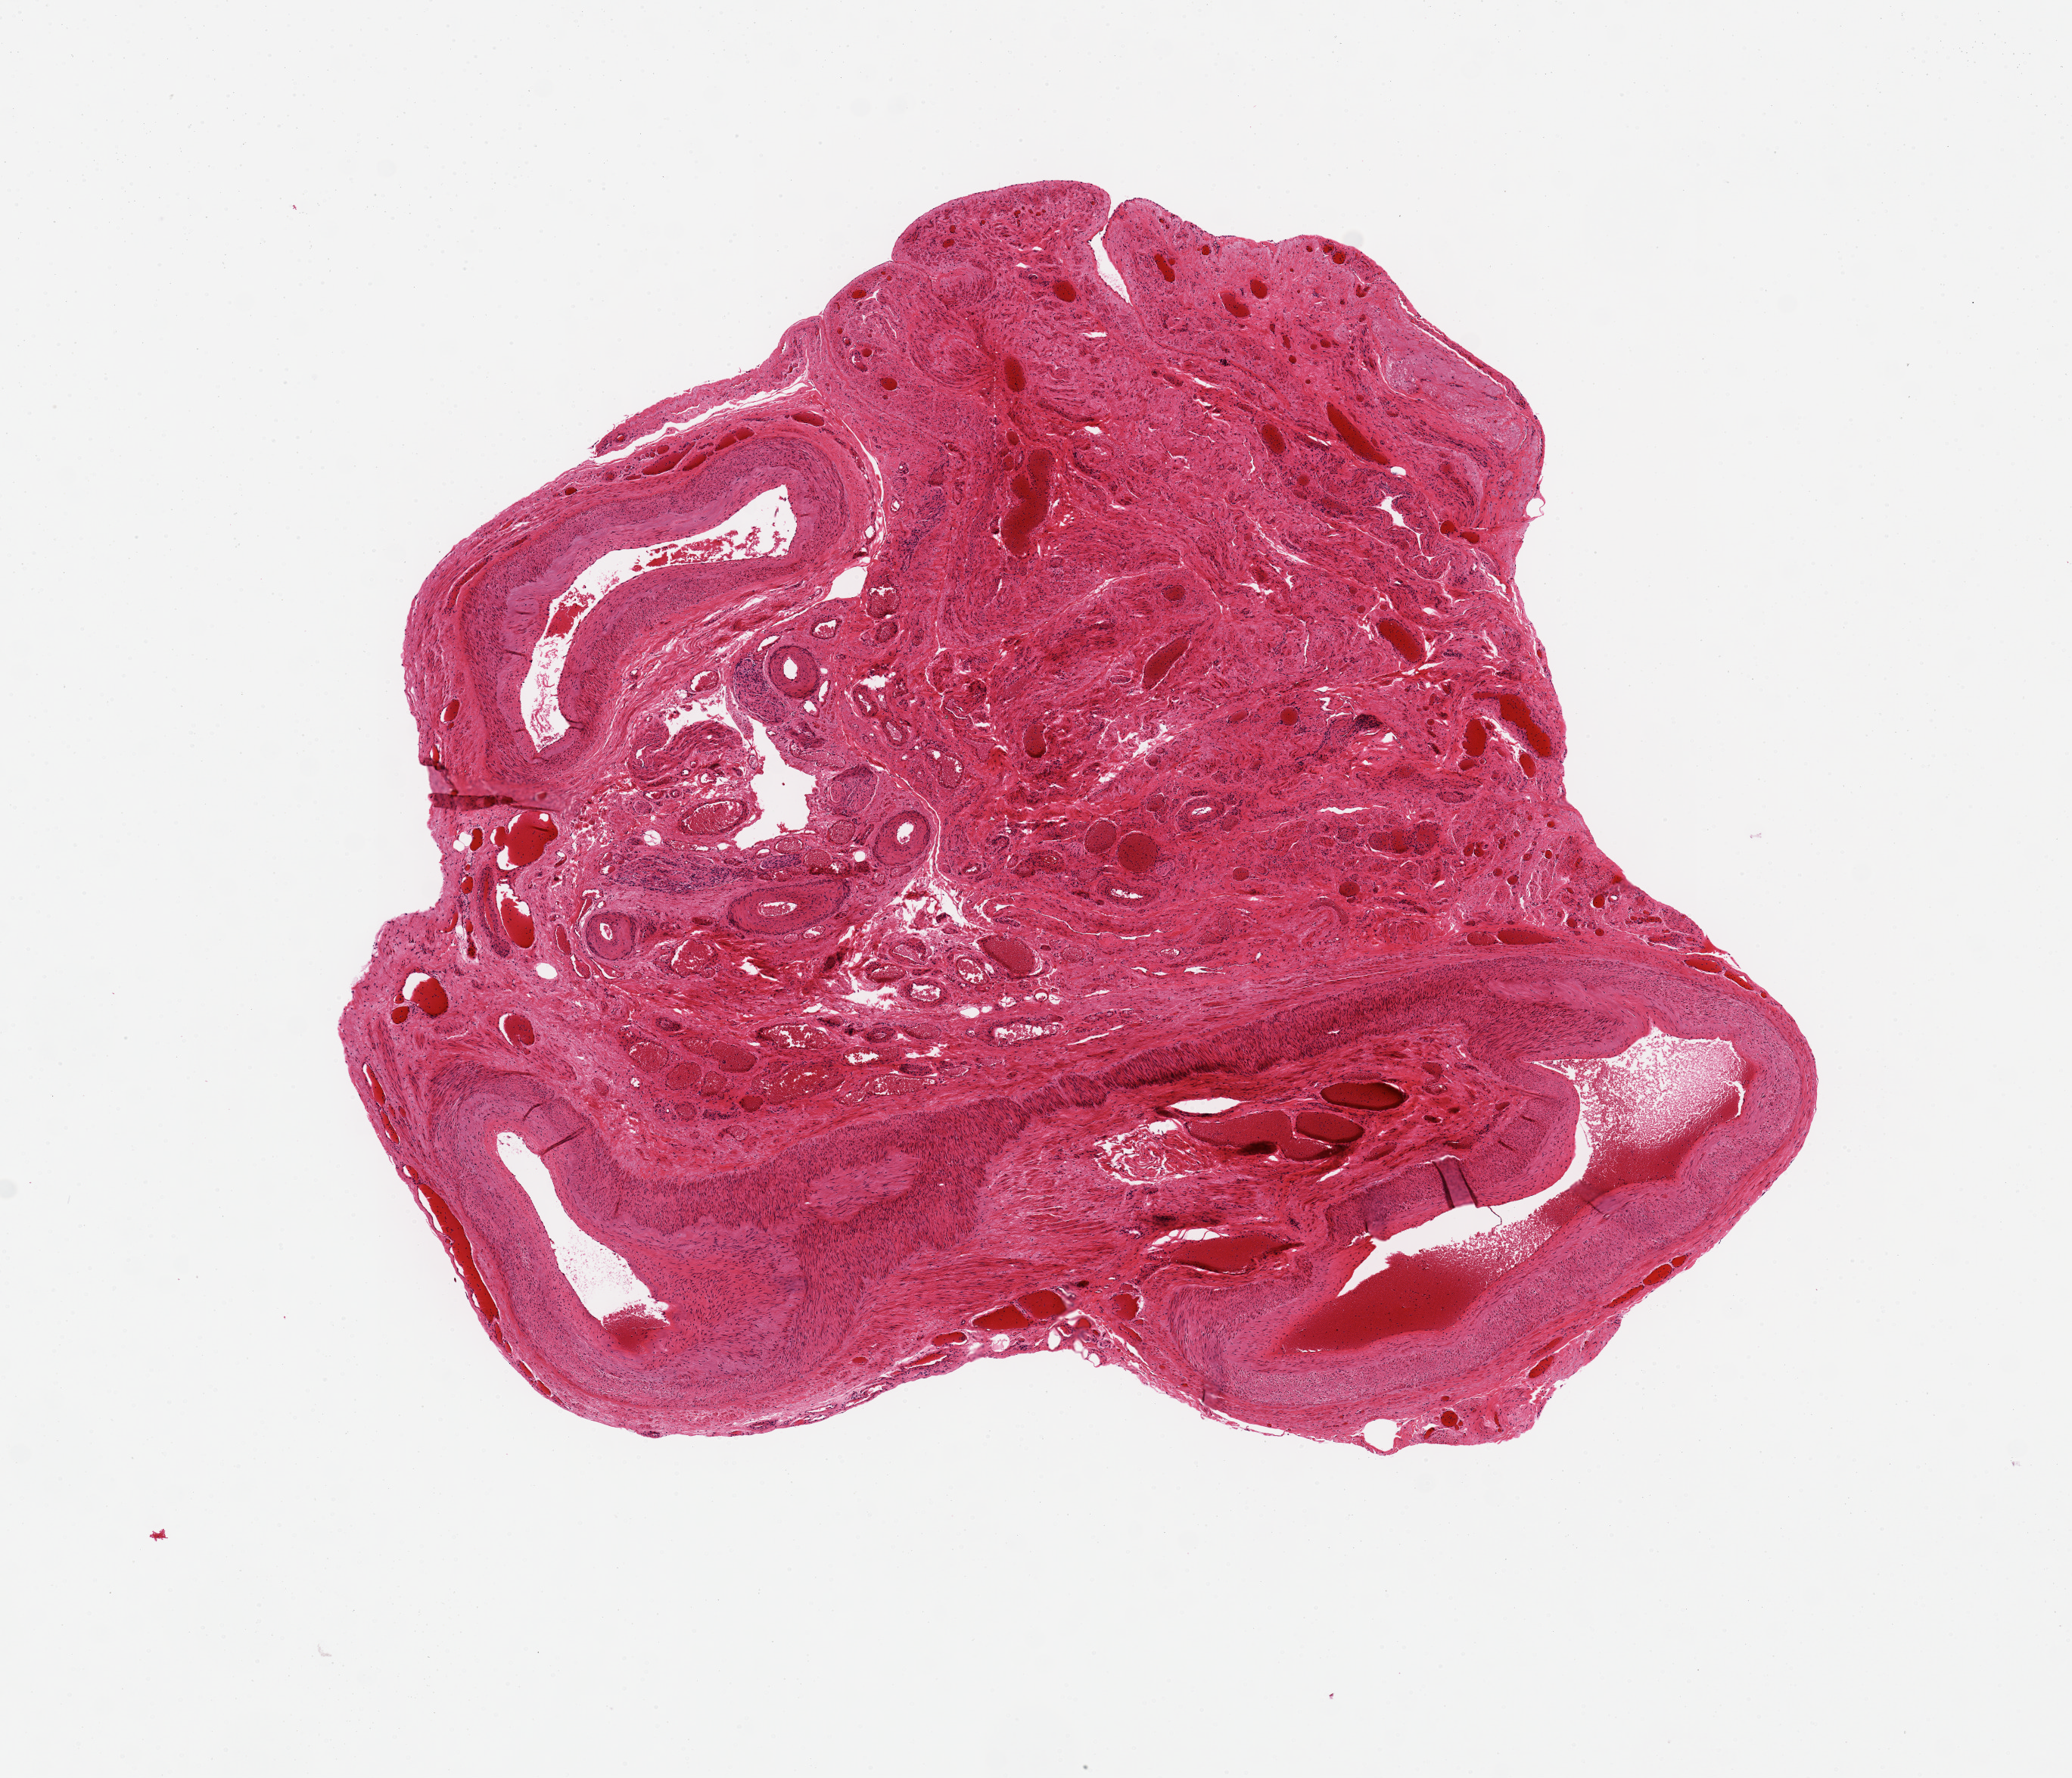
Whole-slide image, haematoxylin and eosin stain, low-resolution overview of the scanned area, about 10.8 x 9.3 mm. PAXgene-fixed paraffin-embedded (PFPE) section. Sampled site (target tissue): fallopian tube. Tissue donor sample.
Reviewer comment on this tissue sample: Not tube; probably broad ligament.